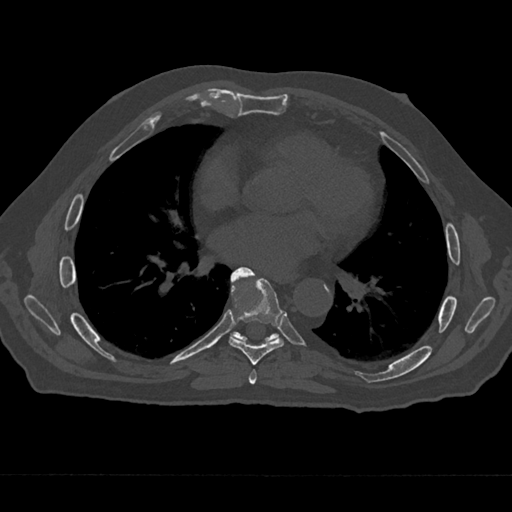
CT including the spine, one axial slice. Bone window (W 1800 / L 400 HU). 0.5 mm slice thickness. 512 × 512 image matrix, field of view 377 × 377 mm. Patient: male, 75 years. Case-level facts recorded for this patient, not image findings: primary cancer: renal.
Structures marked on this image (semi-automatically segmented with operator editing):
- T6 vertebra: bounding box (x1, y1, x2, y2) in pixels: (249, 370, 257, 385)
- T7 vertebra: (229, 267, 284, 365)
- T8 vertebra: (230, 332, 280, 342)